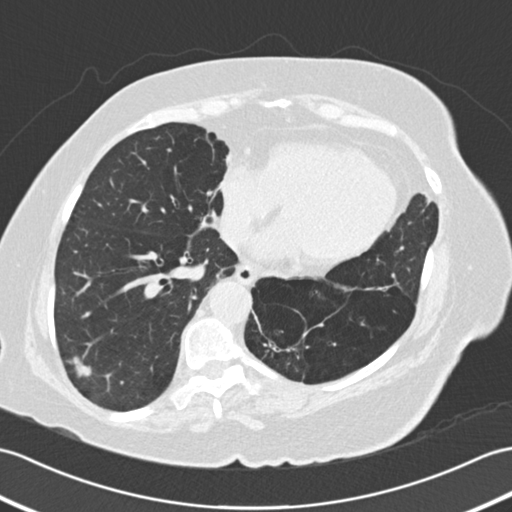
Low-dose screening chest CT, one axial slice; reconstruction kernel B30f; 120 kVp; lung window (W 1500 / L -600 HU); 512 × 512 image matrix.
Outlined on this slice (manually delineated by an expert):
- lesion 1 (tumor, lower lobe of right lung): bounding box <70,355,91,376> (left, top, right, bottom; pixels)